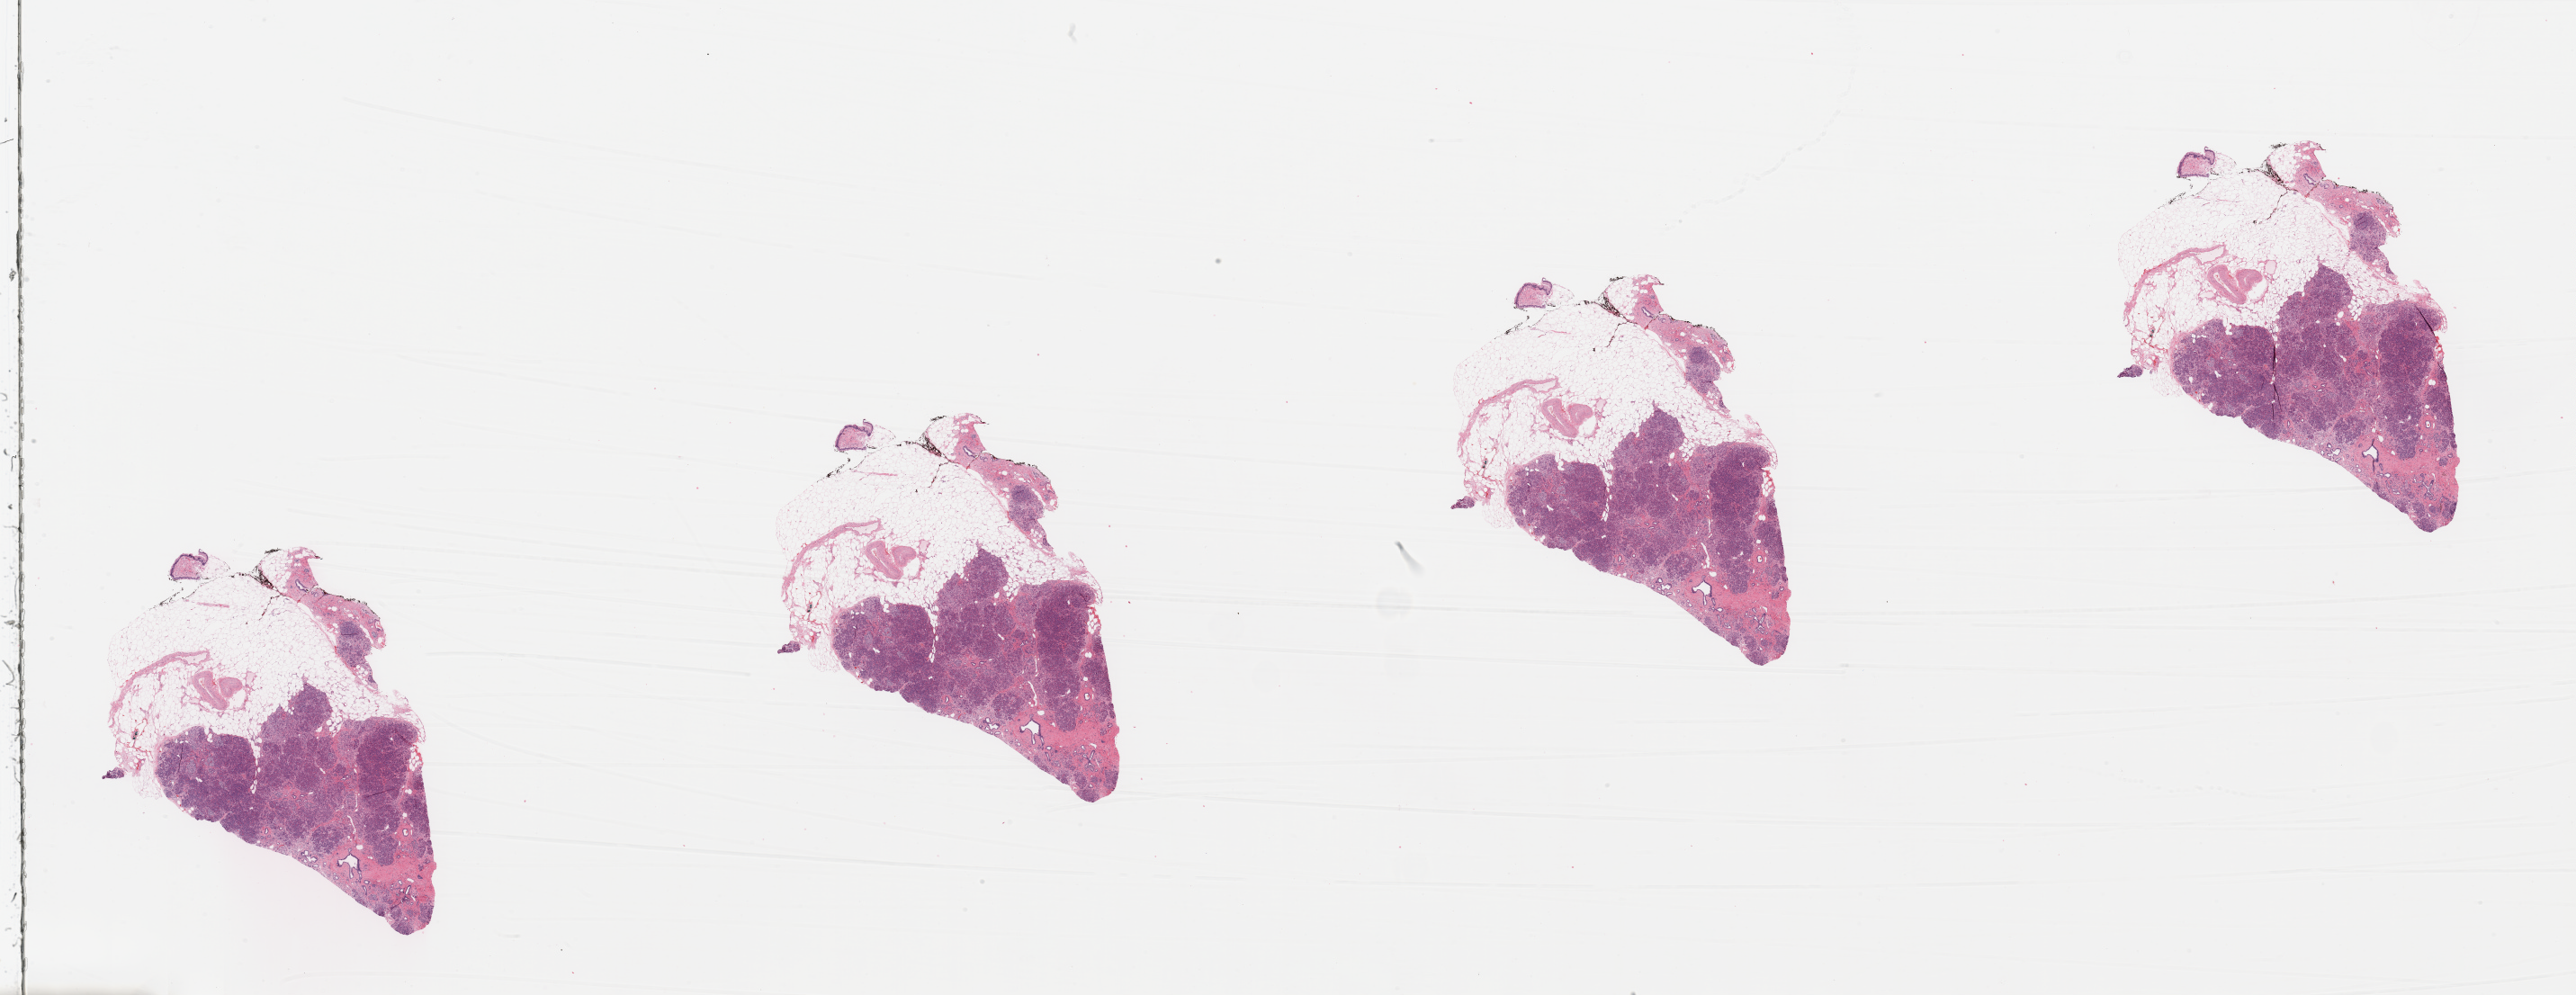
Whole-slide histology image, H&E — shown as a low-resolution overview of the whole scanned area (about 45.3 x 17.5 mm); normal (non-tumour) tissue sample, pancreas. Patient: male, age 71 years.
This section: normal (non-tumour) tissue from the same patient. Patient diagnosis: Infiltrating duct carcinoma, NOS.